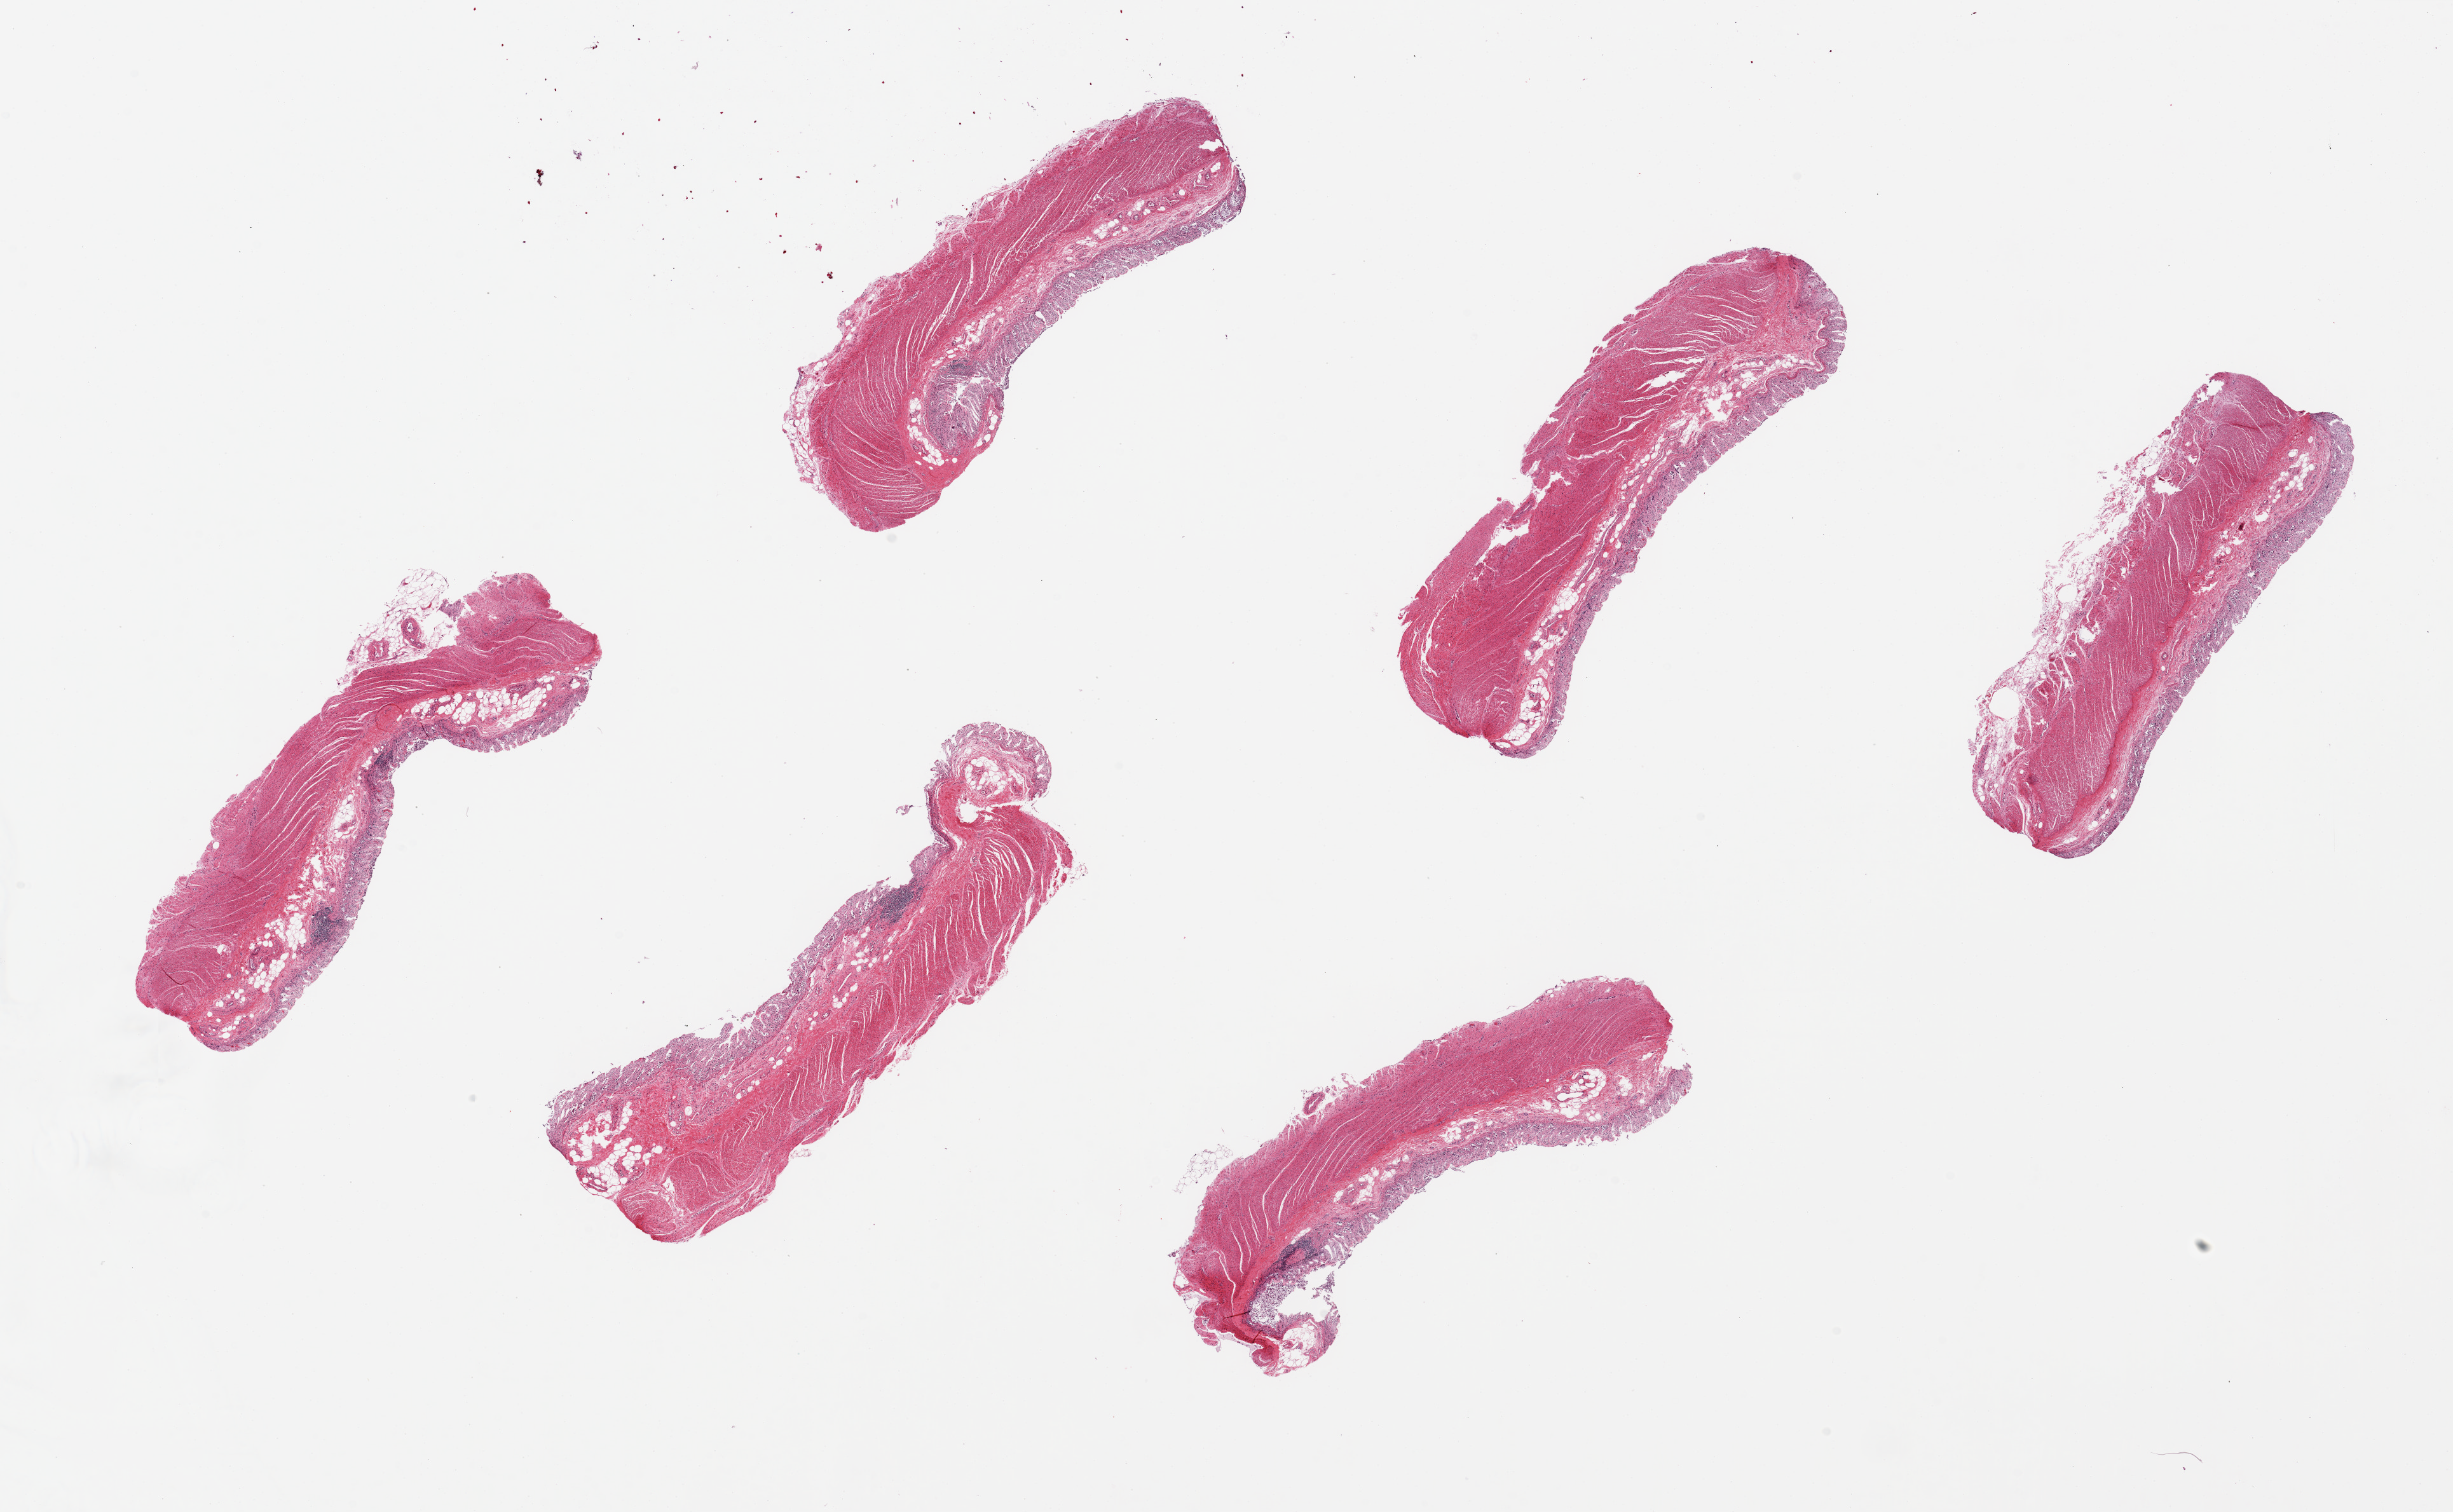
H&E whole-slide image, brightfield — shown as a low-resolution overview of the whole scanned area (about 30.5 x 18.8 mm, acquisition: 20x scan). PAXgene-fixed, paraffin-embedded tissue. Sampled site (target tissue): sigmoid colon. Tissue donor sample.
Review note (as recorded): 6 pieces ~7x2mm, 90% muscle, badly autolyzed.